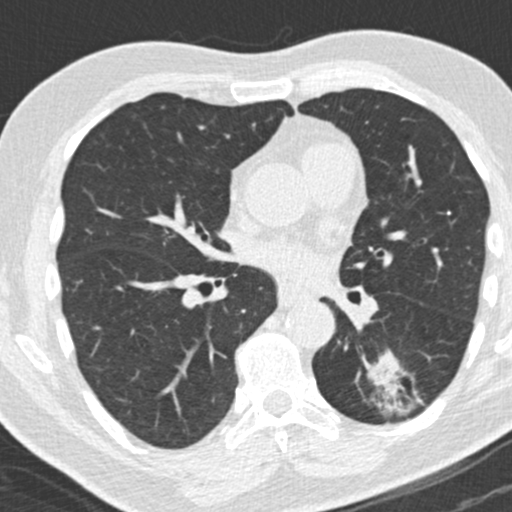
Low-dose screening chest CT, one axial slice. Position 99 of 180 along the scan axis. Reconstruction kernel B30f. Lung window (W 1500 / L -600 HU). 2 mm slice thickness. 512 × 512 image matrix, field of view 300 × 300 mm.
Structures marked on this image (expert manual segmentation):
- lesion 1 (tumor, lower lobe of left lung): bounding box [x1, y1, x2, y2] px = [367, 352, 402, 387]